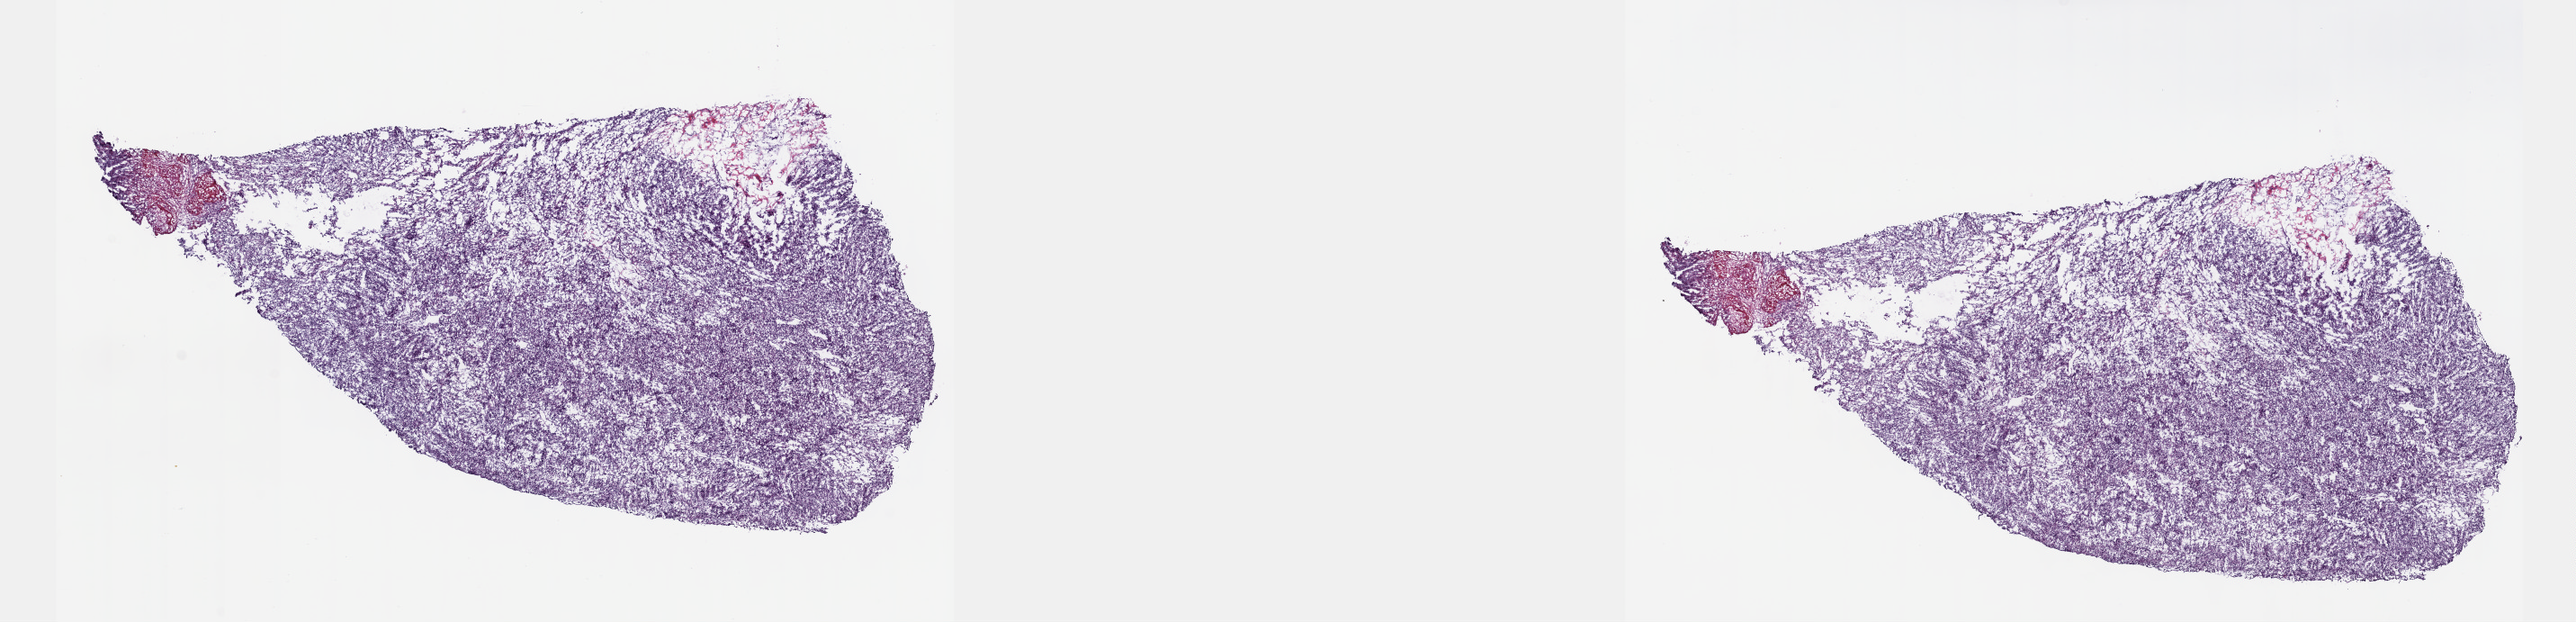
Digitized Hematoxylin and eosin (H&E) stained tissue section (whole slide), low-resolution overview of the scanned area, about 23.1 x 5.6 mm (acquisition: 40x scan), frozen section from the top of the tissue portion, retroperitoneum and peritoneum, primary tumour sample. Female patient; age at initial diagnosis 80 years. Slide review estimates, as recorded: tumour cells 80%, tumour nuclei 80%.
Diagnosis: Dedifferentiated liposarcoma.